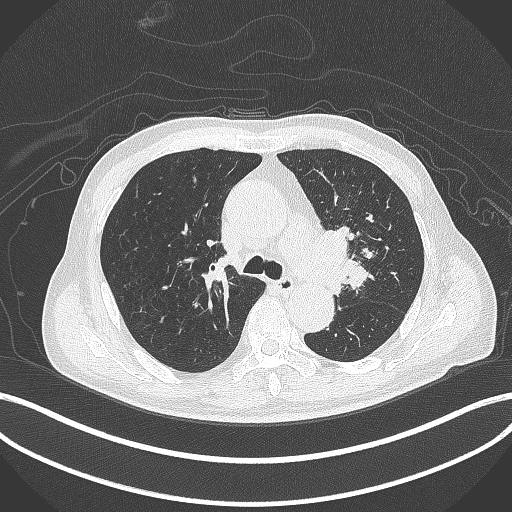
Chest CT, one axial slice. Position 287 of 417 along the scan axis. Reconstruction kernel B70f. 120 kVp. Lung window (W 1500 / L -600 HU). 1 mm slice thickness. 512 × 512 image matrix, field of view 400 × 400 mm. Male patient, age 77 years. Case-level facts recorded for this patient, not image findings: clinical TNM (as recorded): T3 N1 M0.
Outlined on this slice (rectangle marked by the reading radiologist):
- lung tumour (recorded histology: adenocarcinoma): bounding box <310,224,352,293> (left, top, right, bottom; pixels)